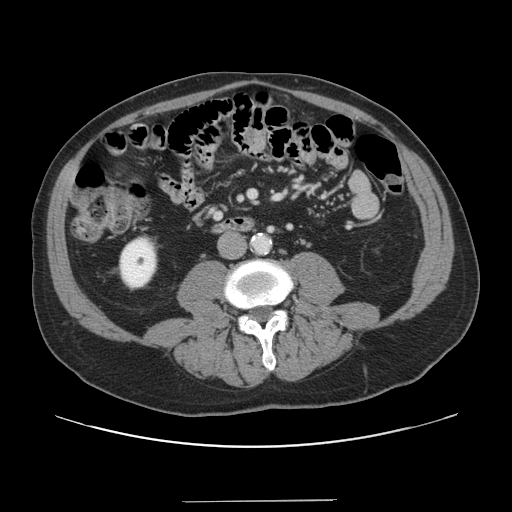
Contrast-enhanced abdominal CT, one axial slice; slice 19 of 151 in the series (ordered by position); soft-tissue window (W 400 / L 40 HU); 2.5 mm slice thickness; 512 × 512 image matrix, field of view 399 × 399 mm. Male patient, age 63 years. Case-level facts recorded for this patient, not image findings: diagnosis: colorectal cancer liver metastases, imaged before liver resection.
Structures marked on this image (manually delineated by an expert):
- portal vein (with intrahepatic branches): bounding box (x1, y1, x2, y2) in pixels: (250, 191, 254, 196)